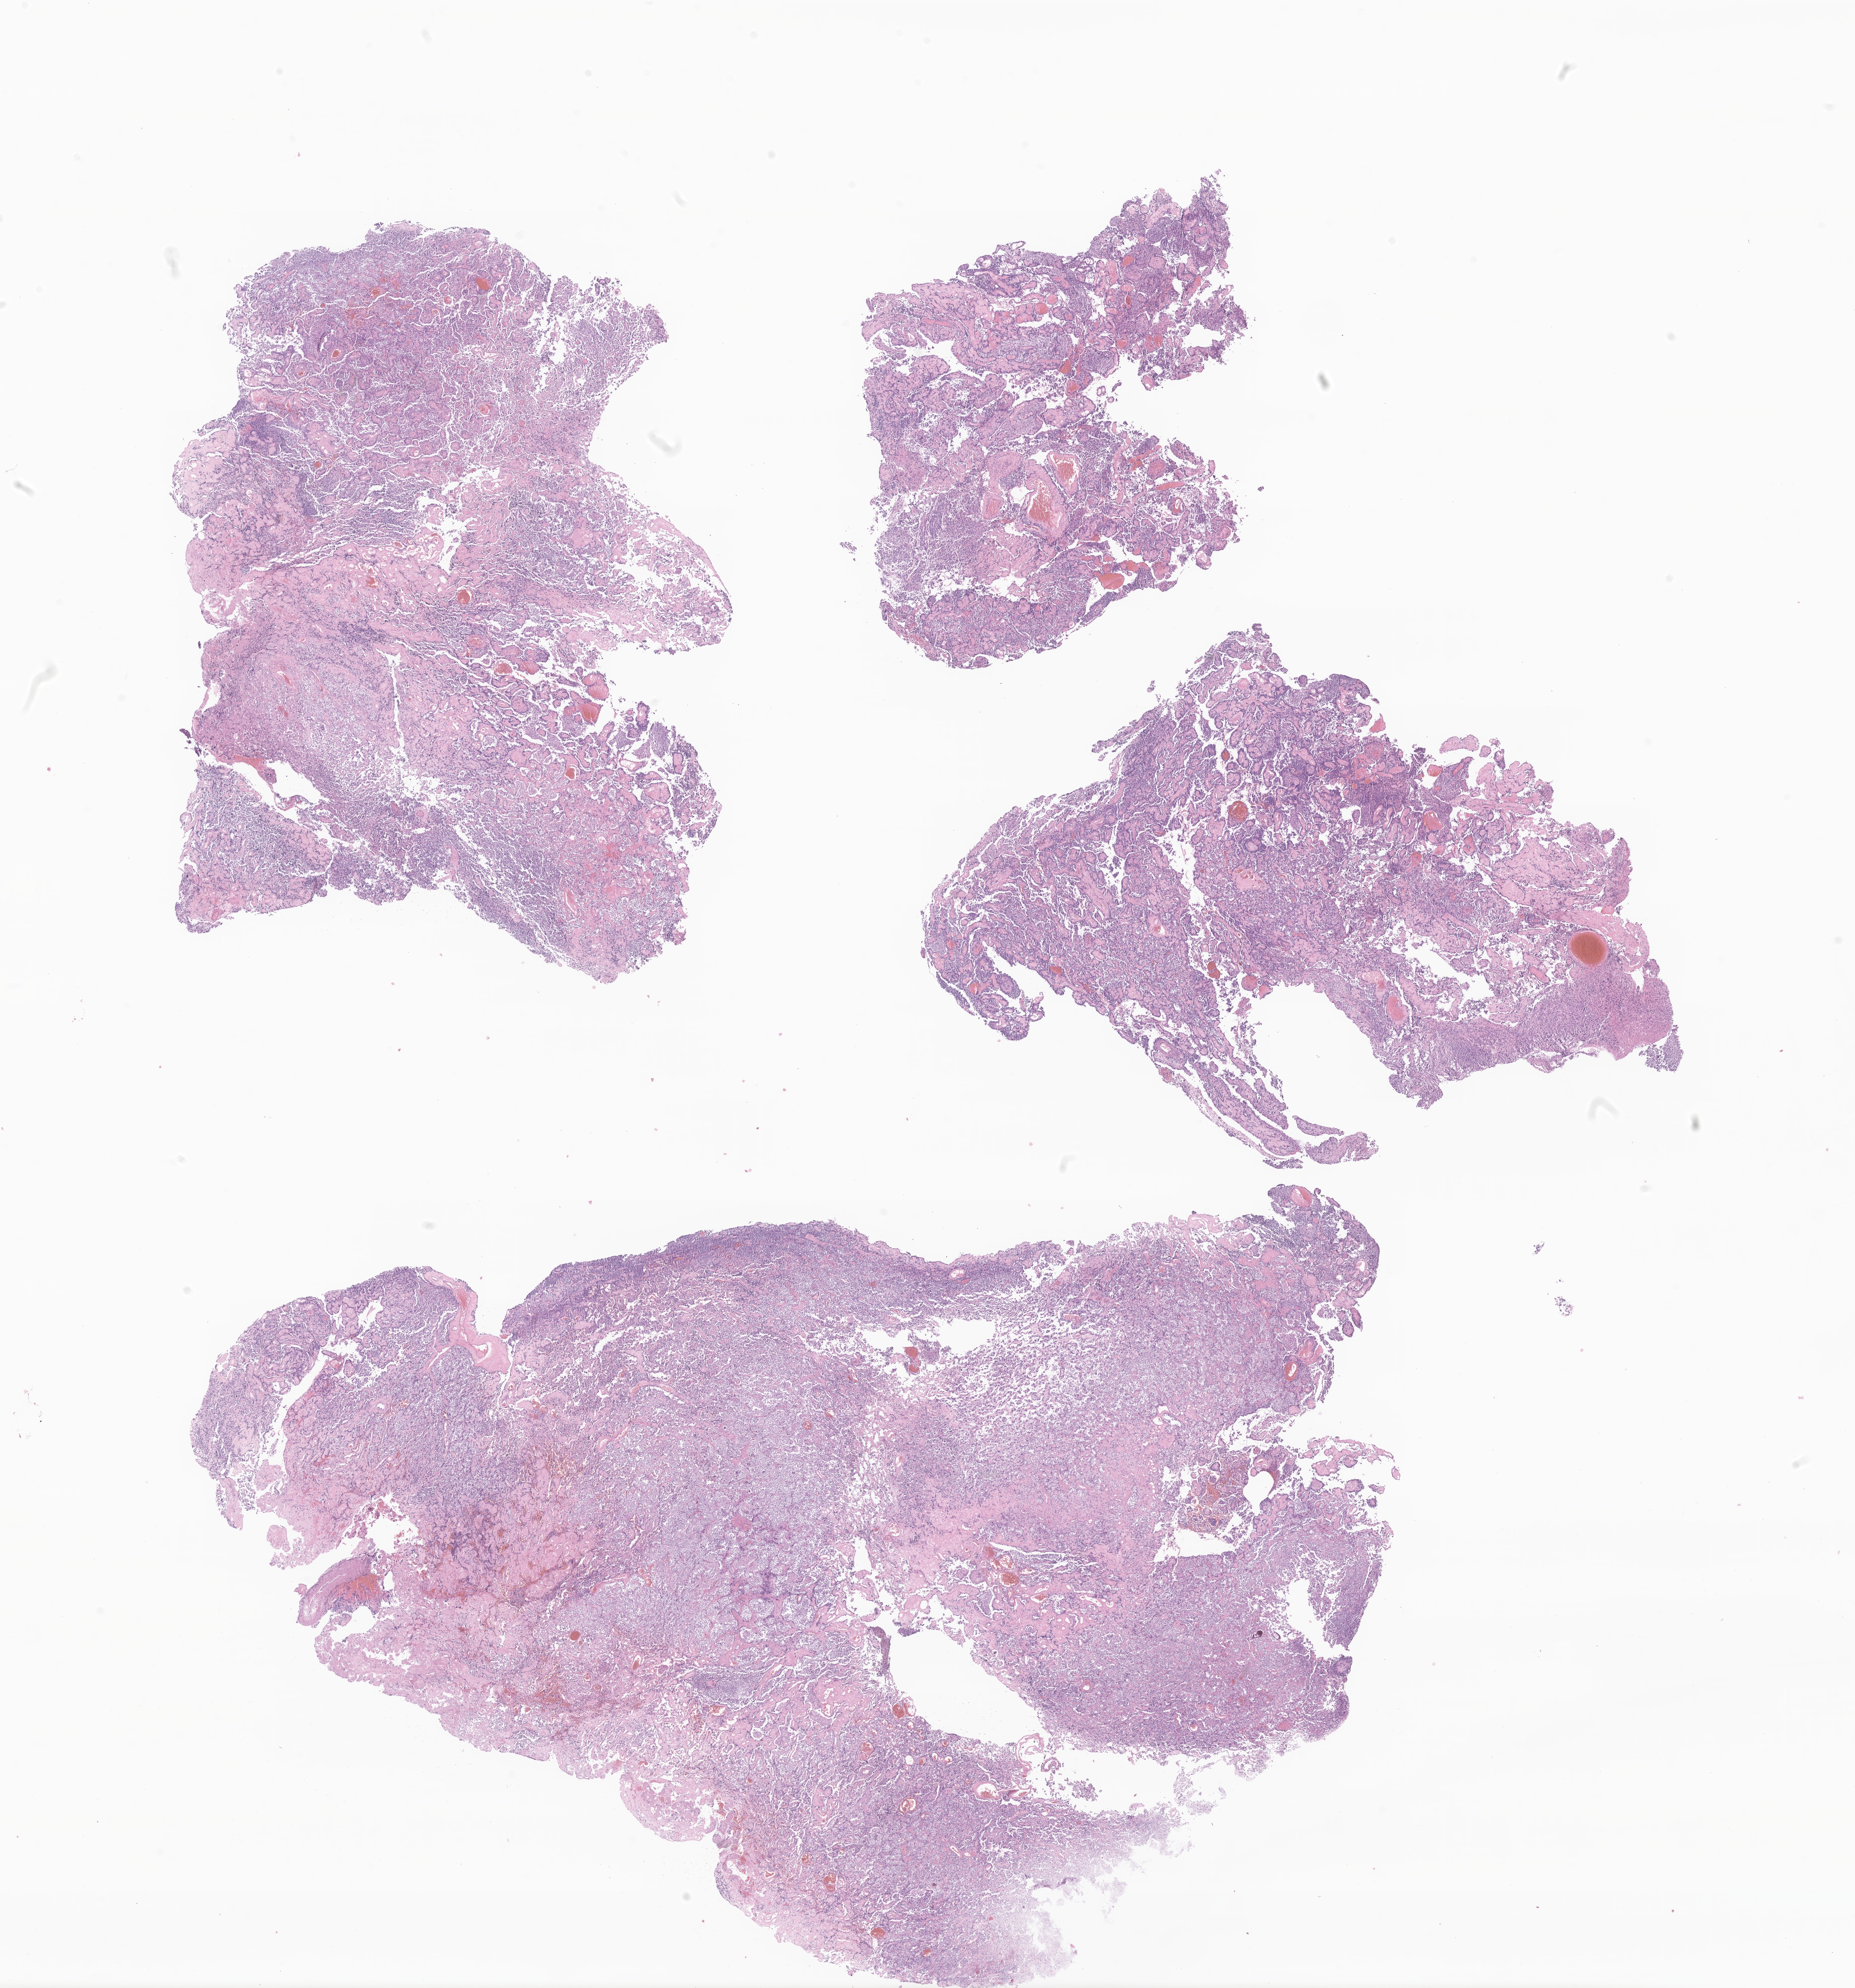
Digitized hematoxylin and eosin (H&E)-stained section of tumor tissue from the occipital lobe, shown as a low-resolution overview of the whole scanned area (about 20.1 x 21.5 mm). Formalin-fixed, paraffin-embedded (FFPE) tissue. Patient: female, age 214 months.
- recorded diagnosis: Tumor cells, uncertain whether benign or malignant